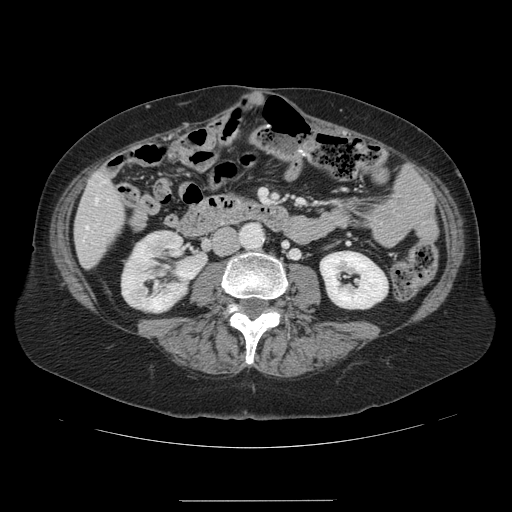
Contrast-enhanced abdominal CT, one axial slice. Position 26 of 141 along the scan axis. Intravenous contrast given. Soft-tissue window (W 400 / L 40 HU). 2.5 mm slice thickness. 512 × 512 image matrix, field of view 393 × 393 mm. Female patient, age 74 years. From the clinical record (not read from this slice): diagnosis: colorectal cancer liver metastases, imaged before liver resection; multiple liver metastases: yes; largest metastasis: 7 cm; disease in both lobes: yes.
Outlined on this slice (expert manual segmentation):
- hepatic veins: box from (x=86, y=199) to (x=97, y=228) px
- liver: (x=76, y=174)–(x=124, y=267)
- planned liver remnant (the part of the liver to remain after resection): (x=80, y=174)–(x=107, y=267)